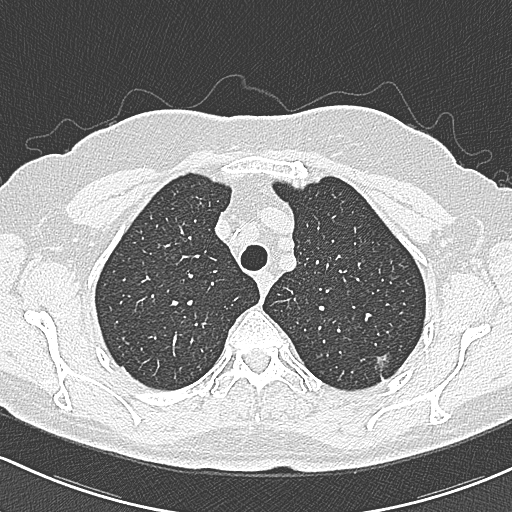
Chest CT (low-dose screening protocol), one axial image, baseline annual screen, lung window (W 1500 / L -600 HU), slice 56 of 312 in the series, 512 × 512 image matrix, field of view 318 × 318 mm. Female participant, aged 65 years at enrolment.
Expert-annotated lung lesion, bounding box (x1, y1, x2, y2) in pixels: (367, 344, 403, 382). The screening reader recorded 3 non-calcified nodules or masses ≥4 mm on this exam; which of them this box marks is not recorded.